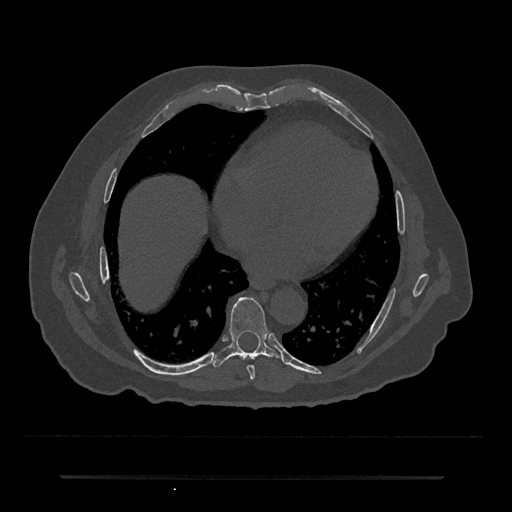
CT including the spine, one axial slice; slice 345 of 797 in the series (ordered by position); bone window (W 1800 / L 400 HU); 0.5 mm slice thickness; 512 × 512 image matrix, field of view 437 × 437 mm. Patient: male, 69 years. Case-level facts recorded for this patient, not image findings: primary cancer: prostate.
Outlined on this slice (semi-automatic segmentation, software-assisted and operator-edited):
- T7 vertebra: bounding box (x1, y1, x2, y2) in pixels: (247, 365, 255, 380)
- T8 vertebra: (212, 297, 281, 367)